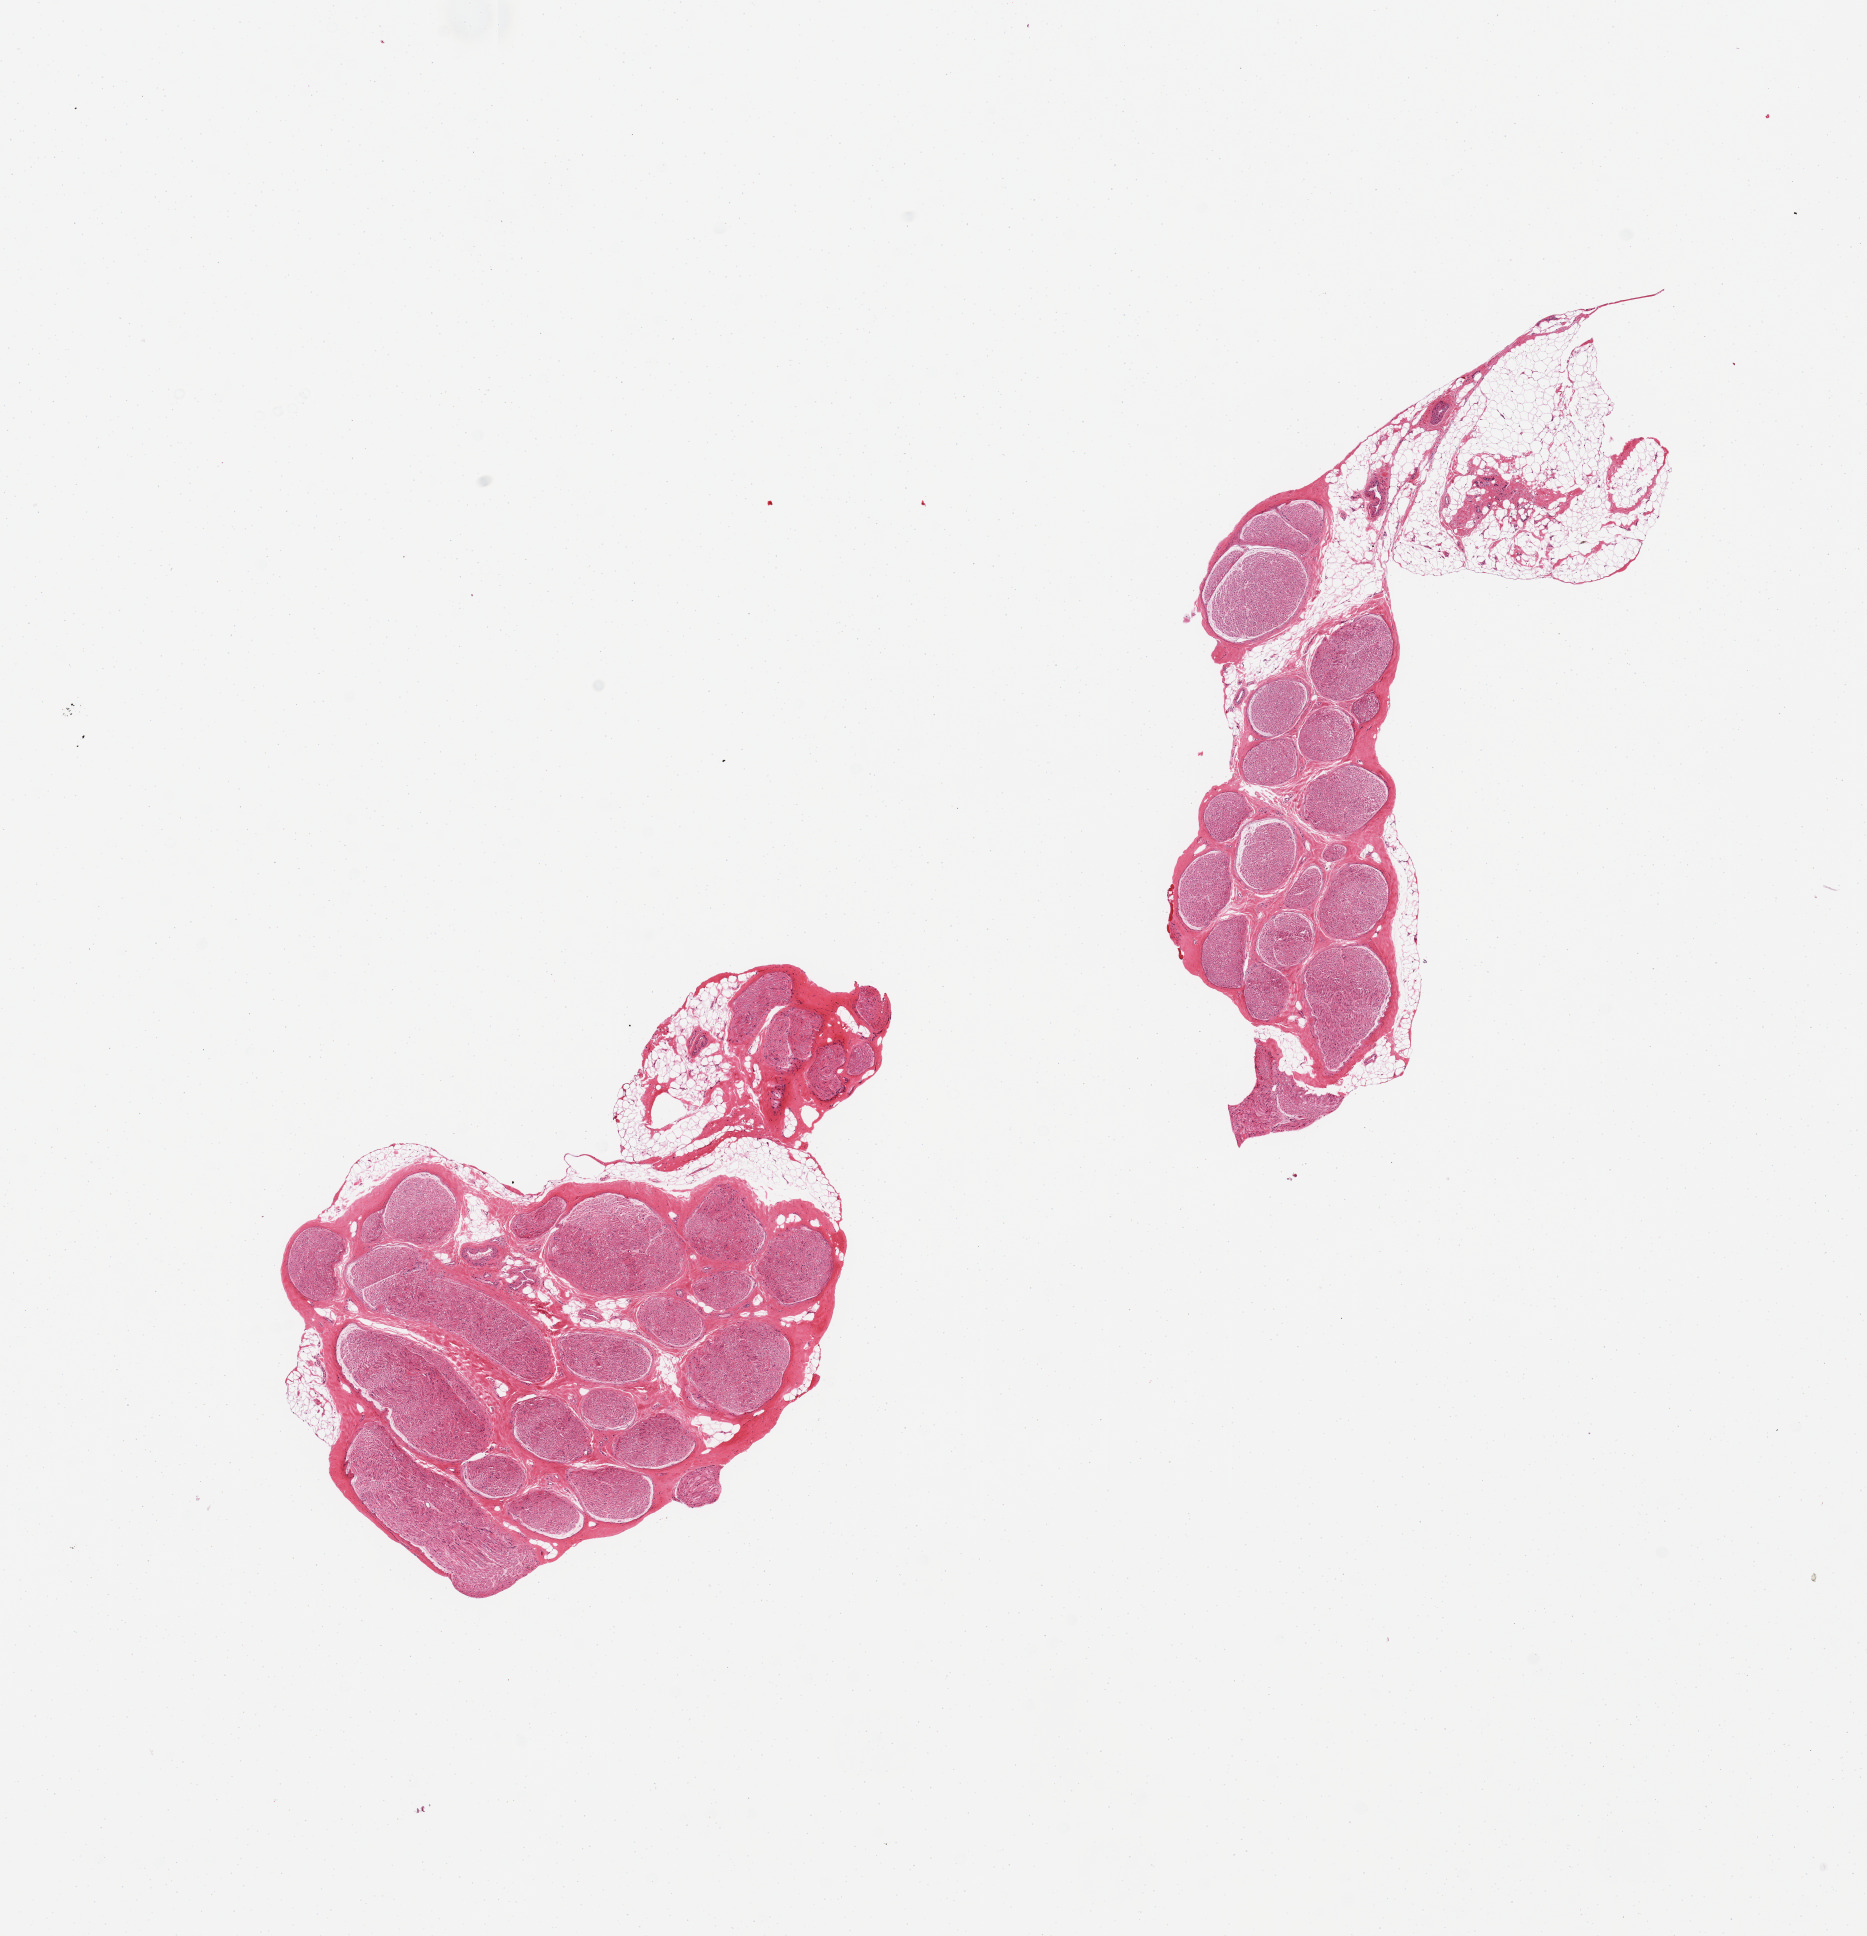
Digitized H&E-stained section — whole scanned area (about 14.8 x 15.3 mm) shown as a low-resolution overview. PAXgene-fixed, paraffin-embedded tissue. Section of tibial nerve (target tissue). Tissue donor sample. Donor sex: male.
Reviewer comment on this tissue sample: 2 pieces, includes 10 and 30% attached fat.